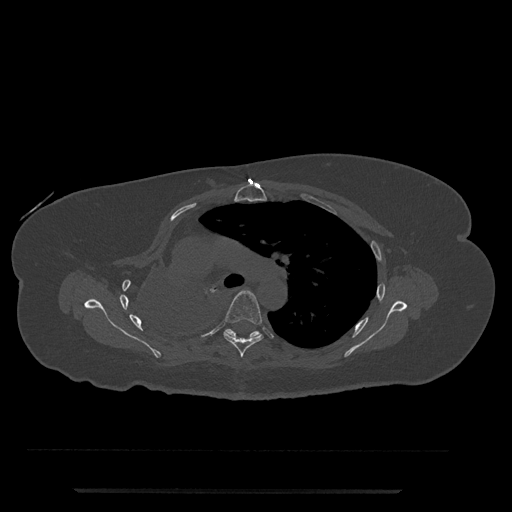
CT including the spine, one axial slice. Position 532 of 797 along the scan axis. Reconstruction kernel Br40s/3. Bone window (W 1800 / L 400 HU). 0.5 mm slice thickness. 512 × 512 image matrix, field of view 440 × 440 mm. Patient: female, 51 years. From the clinical record (not read from this slice): primary cancer: neuro.
Structures marked on this image (semi-automatic segmentation, software-assisted and operator-edited):
- T5 vertebra: box from (x=223, y=290) to (x=263, y=358) px
- T6 vertebra: (x=224, y=329)–(x=261, y=338)